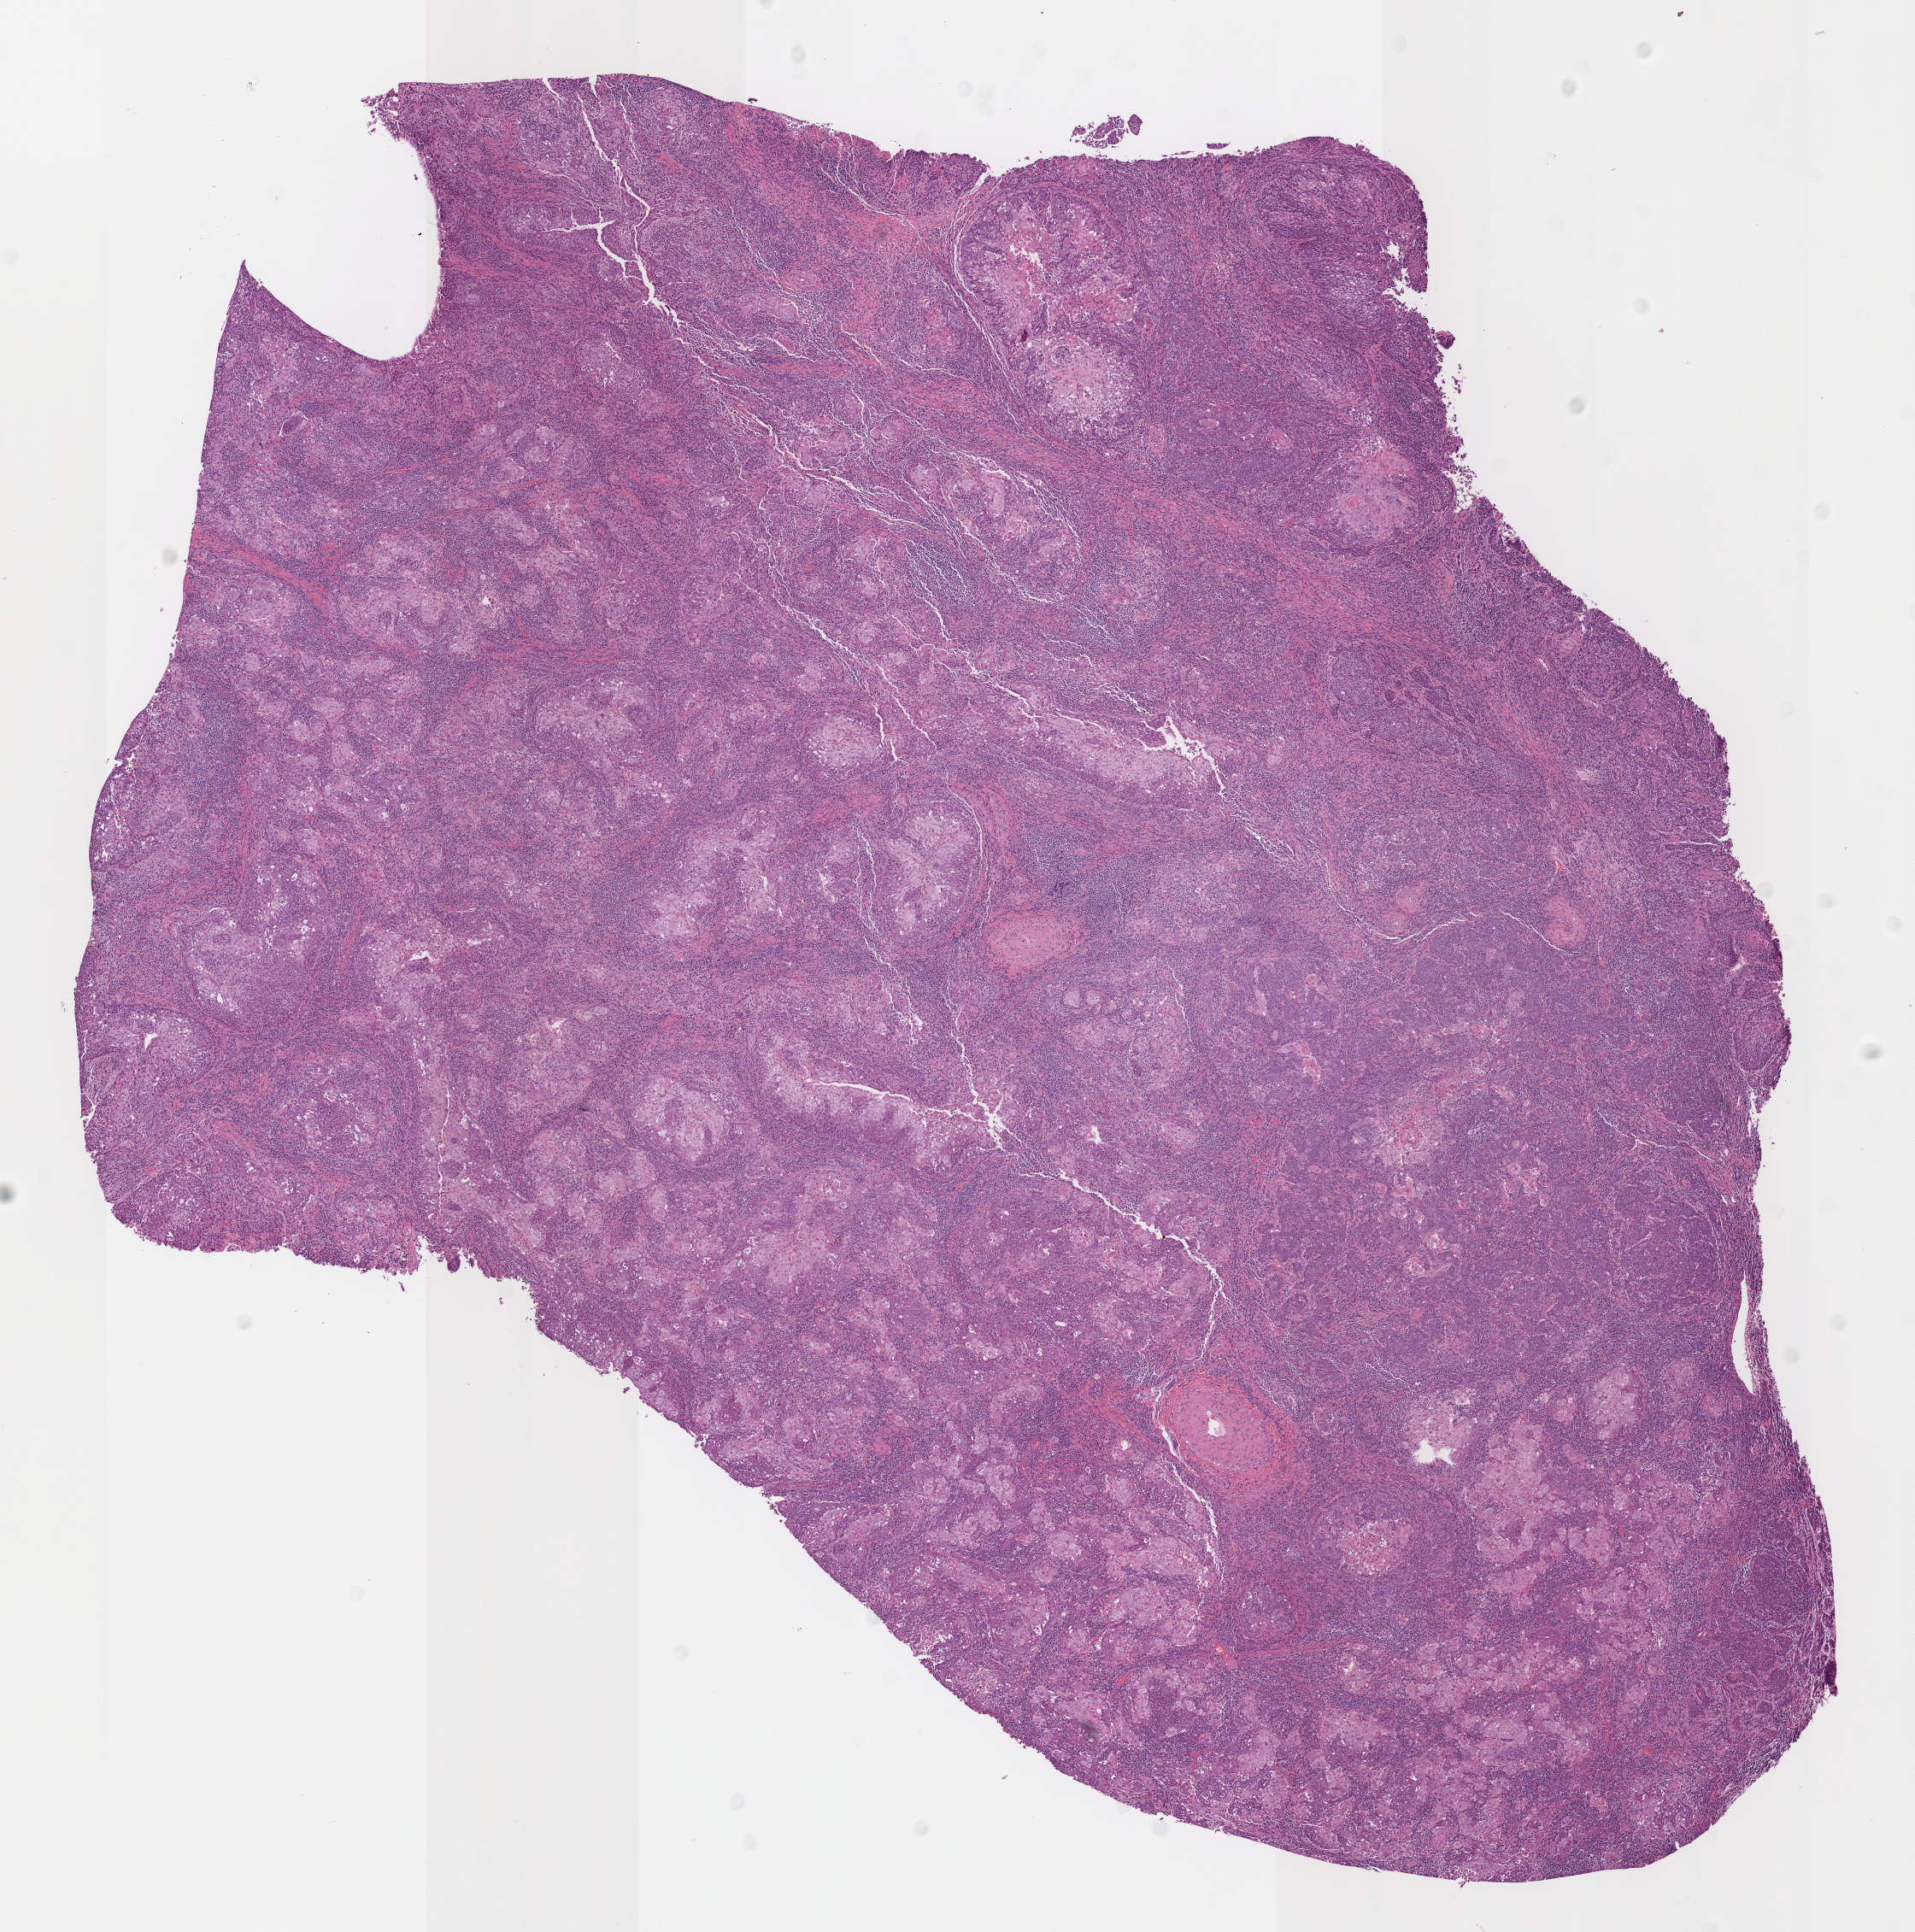
Whole-slide histology image, H&E-stained, whole scanned area (about 8.8 x 8.9 mm, acquisition: 40x scan) shown as a low-resolution overview, FFPE section, sample: primary tumour, cervix. Patient: female, age at initial diagnosis 35 years. Histologic grade: G1 (well differentiated).
Histologic diagnosis: Squamous cell carcinoma, NOS (cervix uteri). Lymph nodes positive (case pathology): 0 of 24 examined. FIGO stage: IB1.